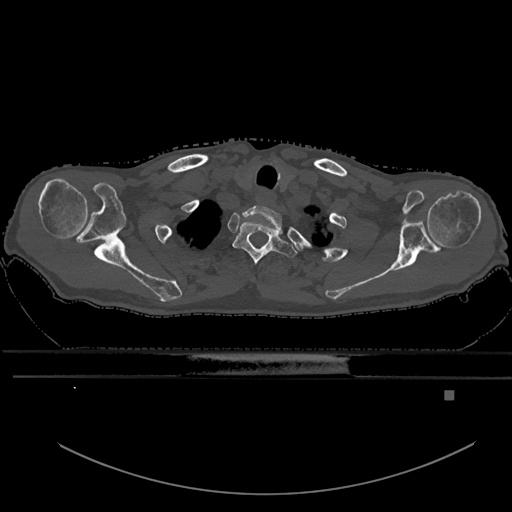
CT including the spine, one axial slice; position 541 of 969 along the scan axis; bone window (W 1800 / L 400 HU); 512 × 512 image matrix. Patient: male, 82 years. Case-level facts recorded for this patient, not image findings: primary cancer: prostate; vertebrae with lytic lesions (as recorded): T11, T9, T8, T2.
Structures marked on this image (semi-automatically segmented with operator editing):
- T1 vertebra: bounding box (x1, y1, x2, y2) in pixels: (233, 221, 297, 266)